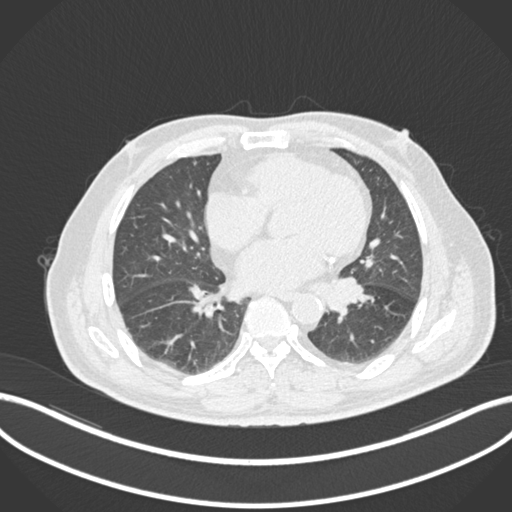
Chest CT, one axial slice; slice 53 of 161 in the series (ordered by position); reconstruction kernel B30f; lung window (W 1500 / L -600 HU); 1 mm slice thickness; 512 × 512 image matrix. Male patient, age 71 years. Case-level facts recorded for this patient, not image findings: clinical TNM (as recorded): T1b N0 M0.
Outlined on this slice (rectangle marked by the reading radiologist):
- lung tumour (recorded histology: squamous cell carcinoma): bounding box (x1, y1, x2, y2) in pixels: (327, 277, 370, 321)